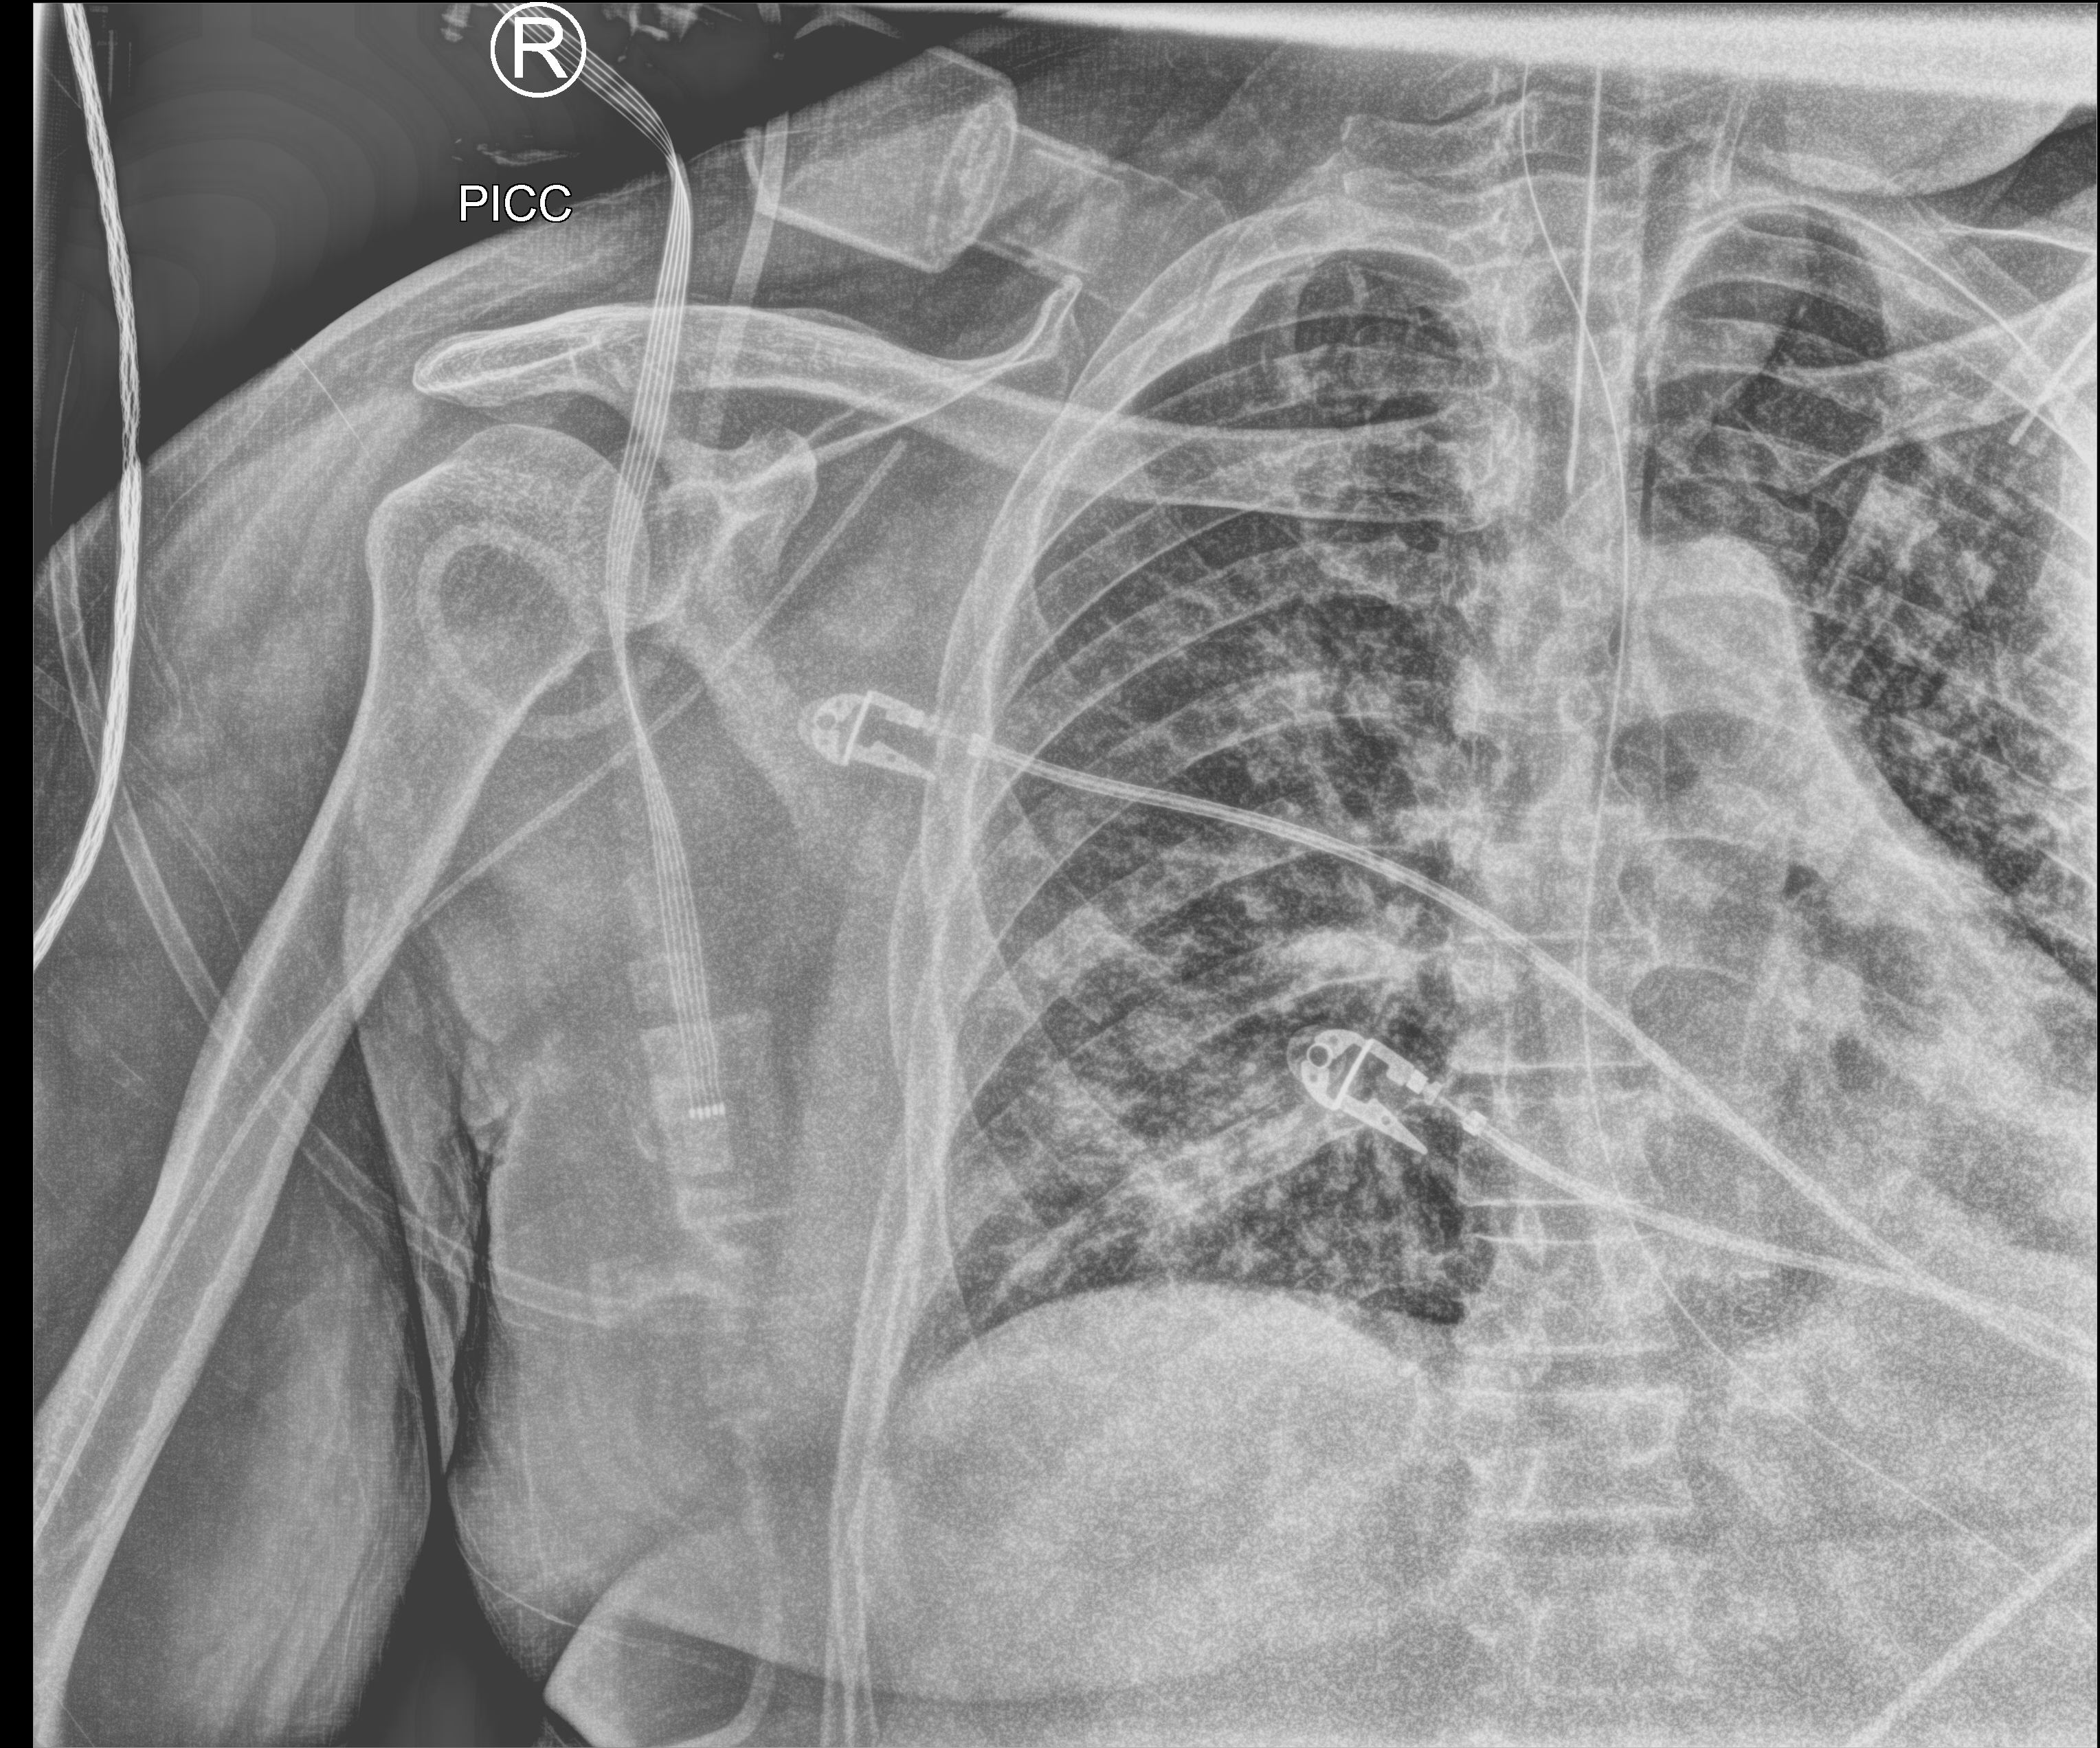
Bedside chest radiograph (computed radiography). Patient hospitalised with COVID-19; male, aged 18–59 years.
From the hospital-stay record, not from the radiograph (when in the stay this image was taken is not recorded): length of hospital stay: 15 days; mechanically ventilated during this hospital stay: yes; admitted to intensive care during this hospital stay: yes.